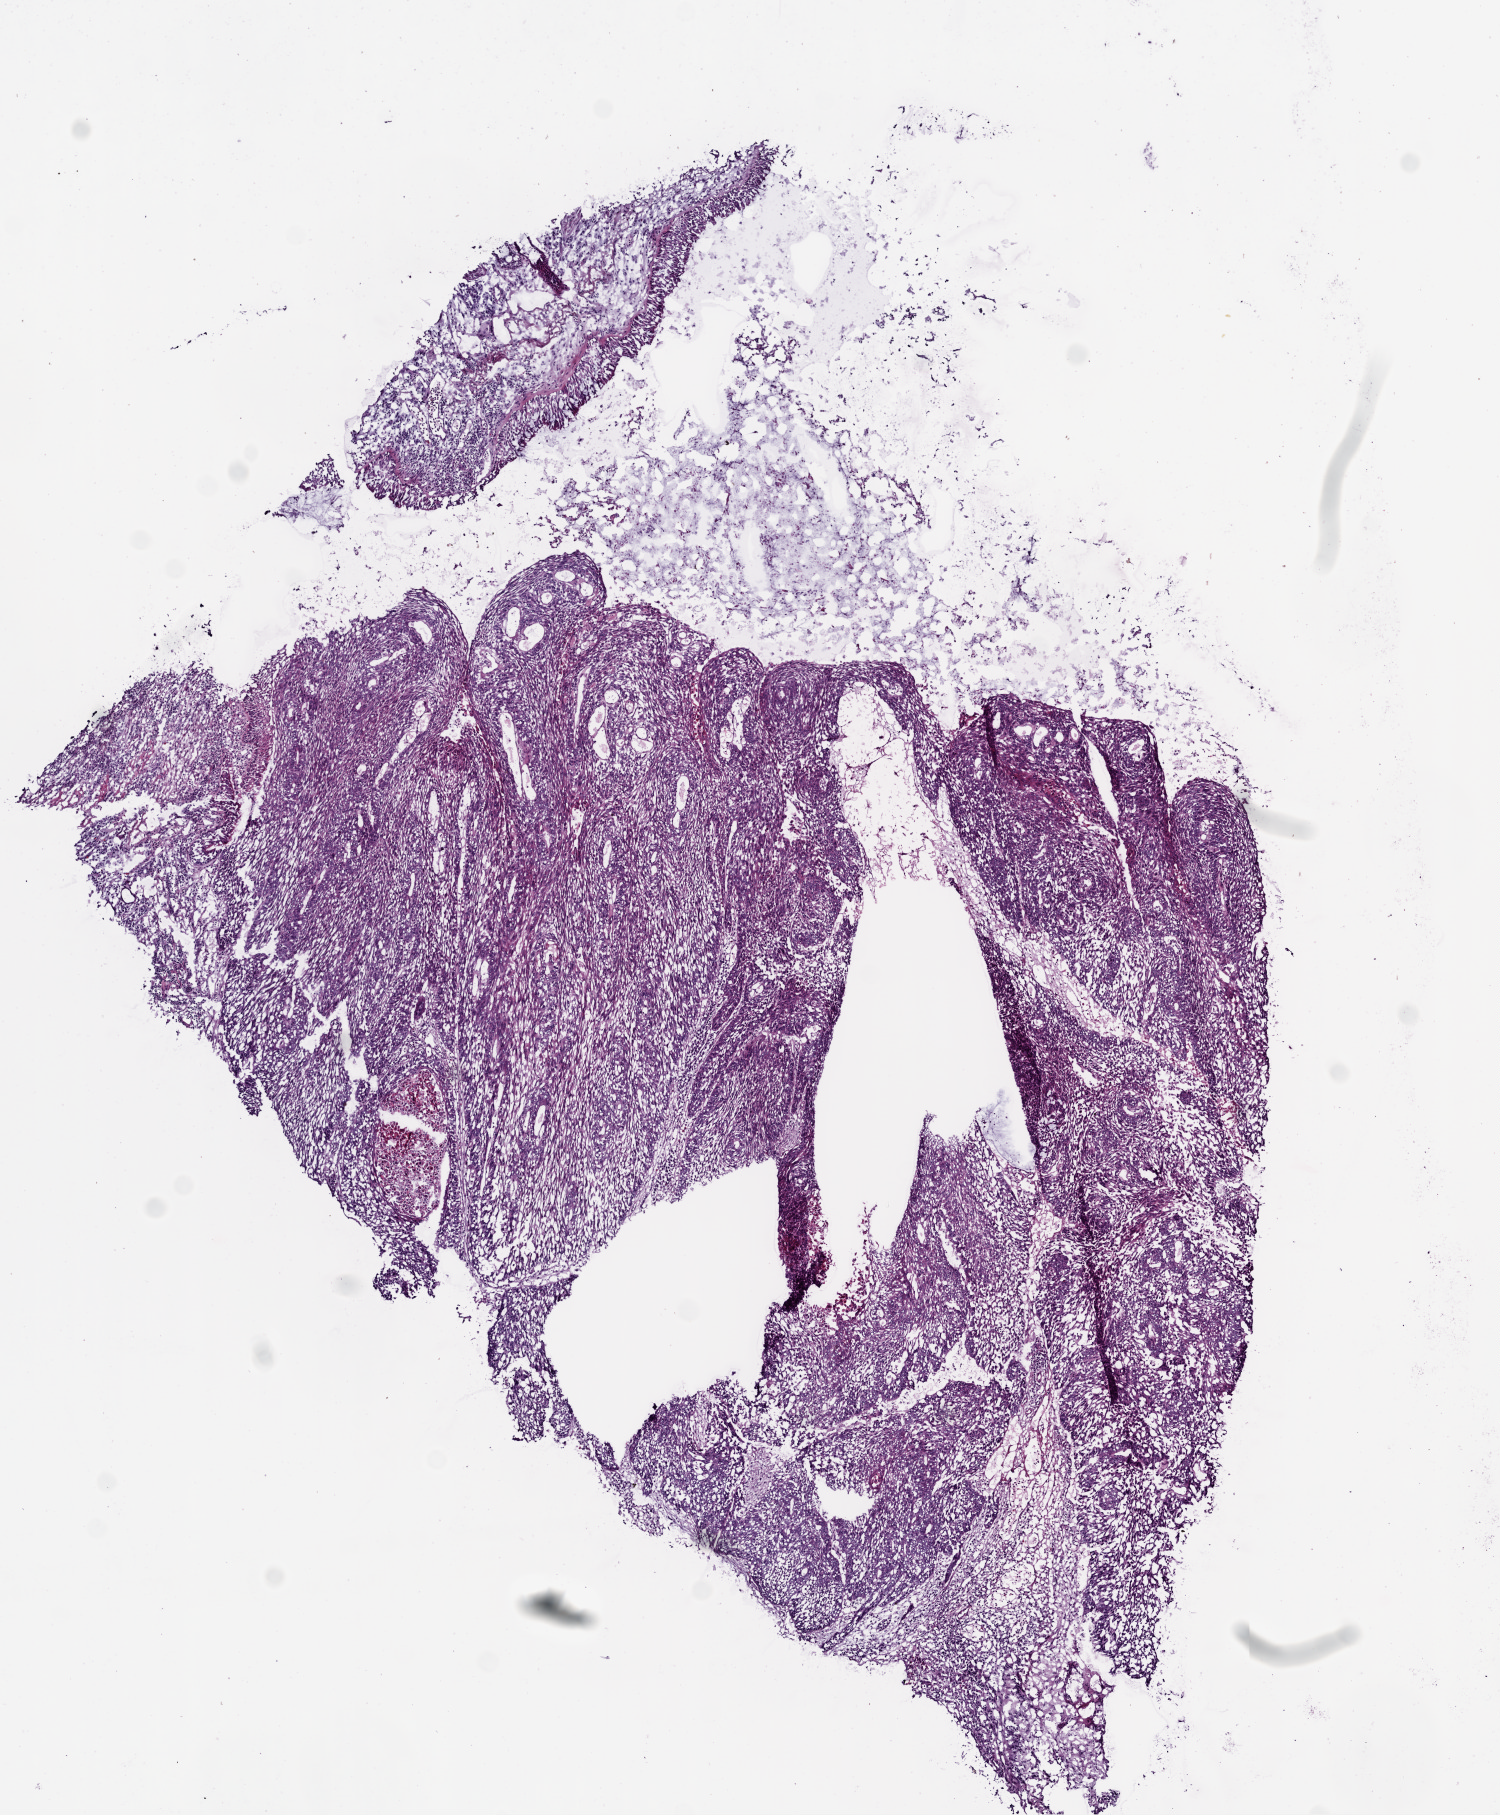
Digitized H&E tissue section (whole slide) — shown as a low-resolution overview of the whole scanned area (about 6.0 x 7.3 mm), frozen section from the bottom of the tissue portion, lung, primary tumour sample. Male patient; age at initial diagnosis 66 years. Slide review estimates, as recorded: tumour cells 75%, tumour nuclei 70%, normal cells 20%, stromal cells 5%, necrosis 0%.
Pathologic diagnosis: Squamous cell carcinoma, NOS (upper lobe, lung). AJCC pathologic stage: IIIA (6th edition).